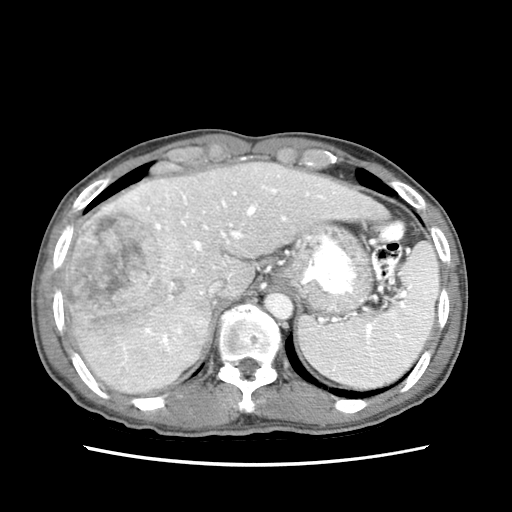
Contrast-enhanced abdominal CT (liver protocol), one axial slice; slice 54 of 79 in the series (ordered by position); reconstruction kernel STANDARD; 120 kVp; soft-tissue window (W 400 / L 40 HU); 2.5 mm slice thickness; 512 × 512 image matrix, field of view 320 × 320 mm. Case-level facts recorded for this patient, not image findings: diagnosis: hepatocellular carcinoma (patient treated with transarterial chemoembolisation; whether this scan precedes or follows treatment is not stated here); TNM stage (as recorded): Stage-IIIB; Child-Pugh class: A; tumour differentiation: moderately differentiated; tumour nodularity: multinodular.
Outlined on this slice (semi-automatic segmentation, software-assisted and operator-edited):
- abdominal aorta: bounding box <264,290,292,319> (left, top, right, bottom; pixels)
- liver parenchyma outside the tumour (the mass and vessels are separate outlines, so this box may not span the whole liver): <60,162,392,394>
- mass: <63,193,187,336>
- liver vessels: <106,173,345,353>